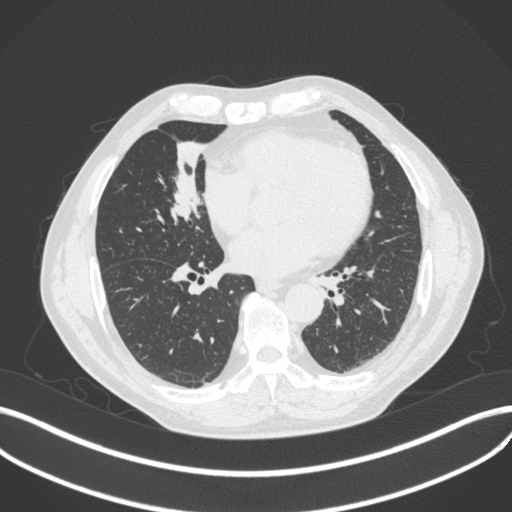
Chest CT, one axial slice. Position 165 of 429 along the scan axis. Lung window (W 1500 / L -600 HU). 1 mm slice thickness. 512 × 512 image matrix, field of view 400 × 400 mm. Male patient, age 61 years. From the clinical record (not read from this slice): clinical TNM (as recorded): T2b N1 M0.
Outlined on this slice (rectangle marked by the reading radiologist):
- lung tumour (recorded histology: squamous cell carcinoma): bounding box (x1, y1, x2, y2) in pixels: (165, 165, 205, 224)